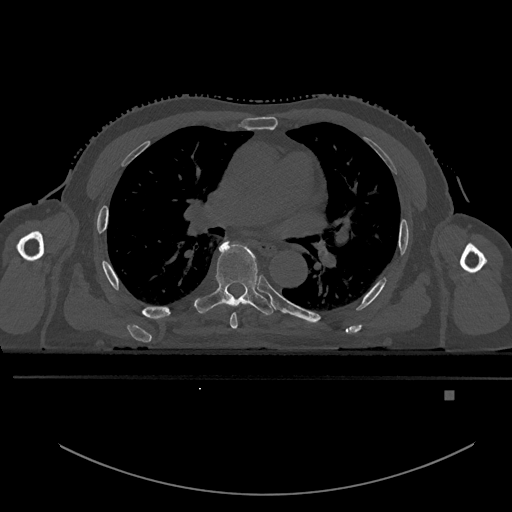
CT including the spine, one axial slice; slice 320 of 969 in the series (ordered by position); bone window (W 1800 / L 400 HU); 0.5 mm slice thickness; 512 × 512 image matrix. Patient: male, 82 years. From the clinical record (not read from this slice): primary cancer: prostate; vertebrae with lytic lesions (as recorded): T11, T9, T8, T2.
Structures marked on this image (semi-automatic segmentation, software-assisted and operator-edited):
- T5 vertebra: bounding box [x1, y1, x2, y2] px = [230, 312, 238, 329]
- T6 vertebra: [193, 238, 274, 315]